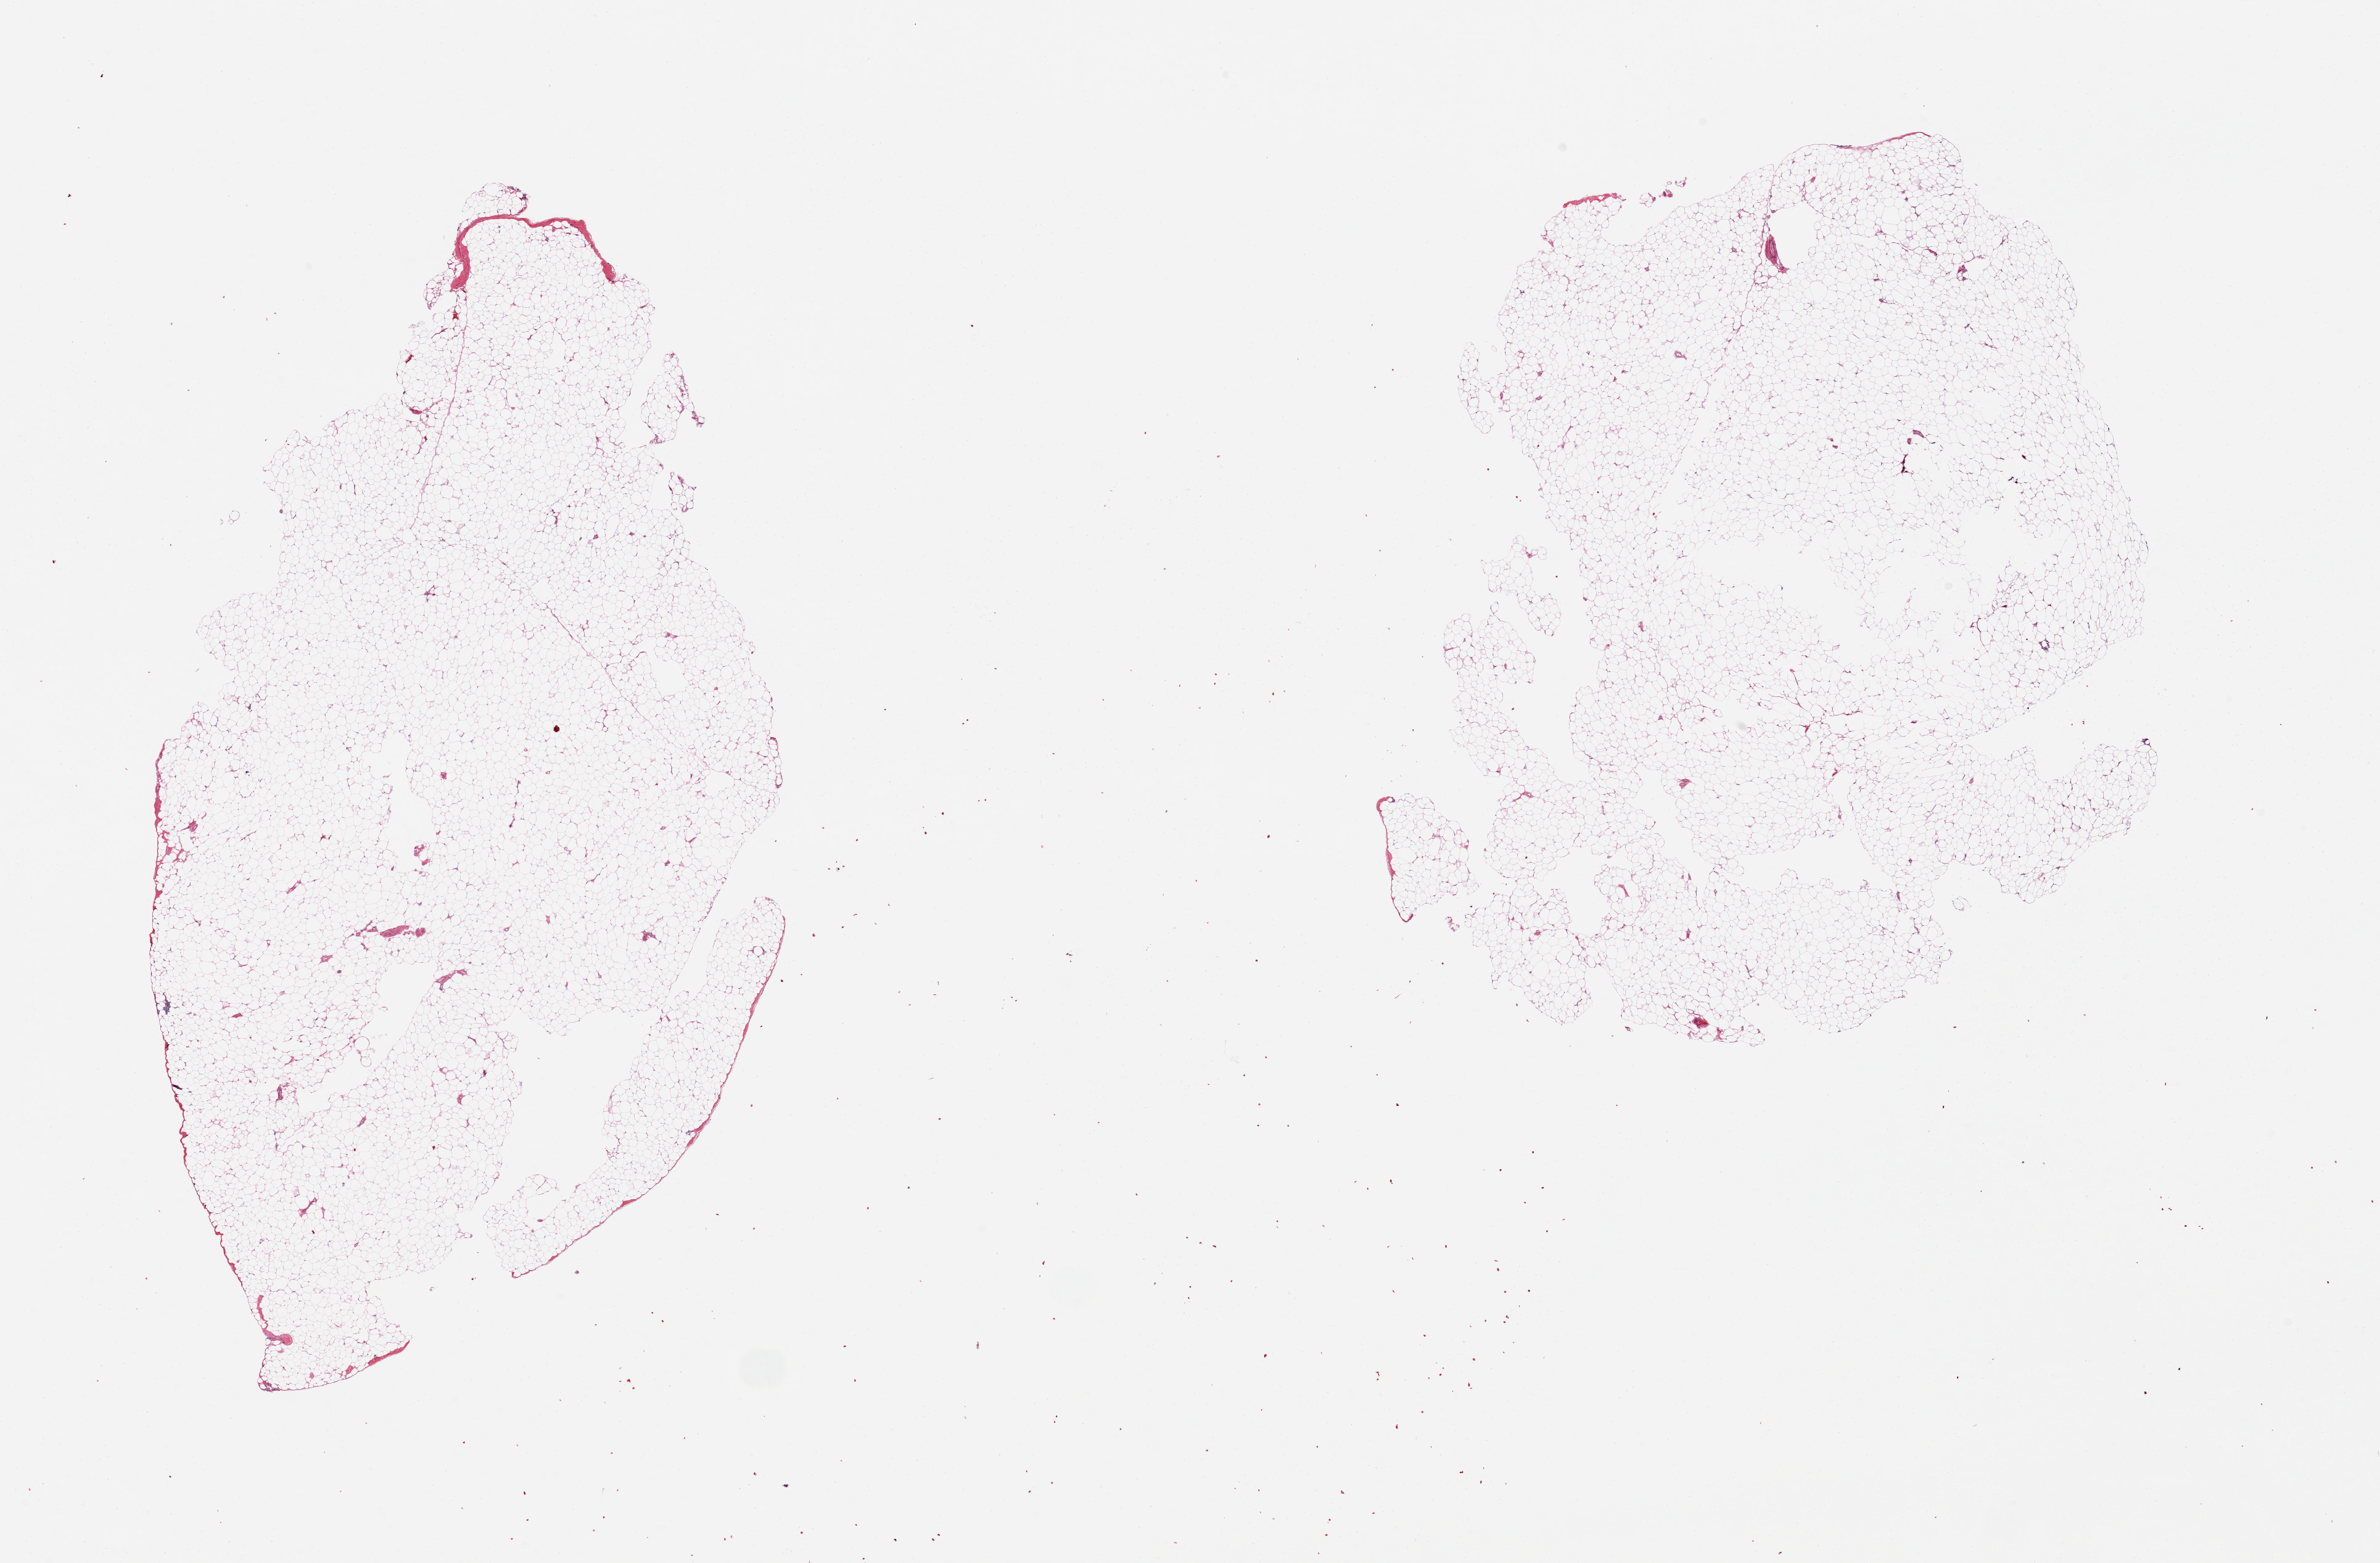
H&E whole-slide image, shown as a low-resolution overview of the whole scanned area (about 30.5 x 20.0 mm, acquisition: 20x scan); PAXgene-fixed paraffin-embedded (PFPE) section; sampled site (target tissue): omentum; donor tissue sample.
Reviewer comment on this tissue sample: 2 pieces, all fat.